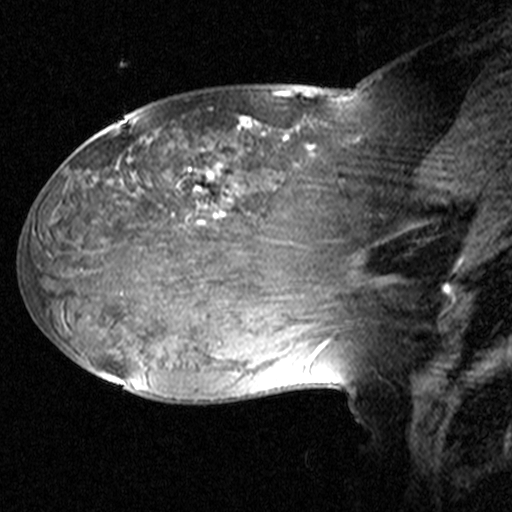
Breast MRI (dynamic contrast-enhanced), one sagittal slice; position 23 of 44 along the scan axis; dynamic contrast-enhanced study with each time point stored as its own series, time point 2 of 3 at this slice position (early post-contrast, ordered by acquisition time); 1.5 T; TE 4.5 ms, TR 11 ms; 3 mm slice thickness; 512 × 512 image matrix, field of view 240 × 240 mm. Female patient, age 38 years. From the clinical record (not read from this slice): setting: breast cancer imaged before/during neoadjuvant chemotherapy; receptor status: HR-positive, HER2-negative.
Structures marked on this image (semi-automatically segmented with operator editing):
- analysis volume of interest (the breast-tissue region the enhancement analysis was run in; not a lesion): bounding box [x1, y1, x2, y2] px = [124, 106, 405, 245]
- tumour enhancement mask (voxels above the 90 % enhancement threshold inside the analysis volume of interest): [194, 117, 253, 223]